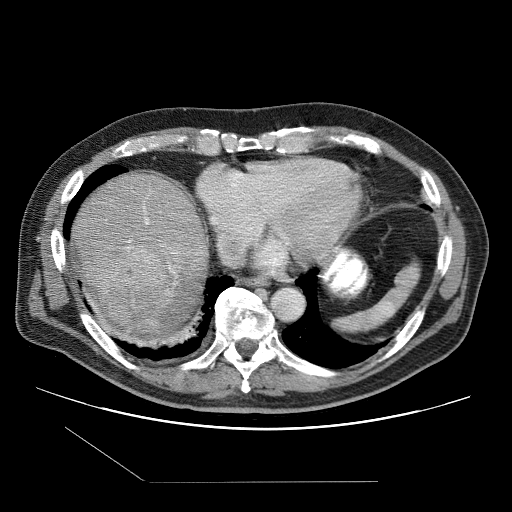
Contrast-enhanced abdominal CT (liver protocol), one axial slice; position 93 of 109 along the scan axis; reconstruction kernel STANDARD; one of 2 acquisitions stored at this slice position; soft-tissue window (W 400 / L 40 HU); 2.5 mm slice thickness; 512 × 512 image matrix, field of view 400 × 400 mm. From the clinical record (not read from this slice): diagnosis: hepatocellular carcinoma (patient treated with transarterial chemoembolisation; whether this scan precedes or follows treatment is not stated here); TNM stage (as recorded): Stage-IIIB; Child-Pugh class: A.
Structures marked on this image (semi-automatic segmentation, software-assisted and operator-edited):
- liver parenchyma outside the tumour (the mass and vessels are separate outlines, so this box may not span the whole liver): bounding box <70,172,206,344> (left, top, right, bottom; pixels)
- mass: <82,247,171,328>
- liver vessels: <127,206,179,254>